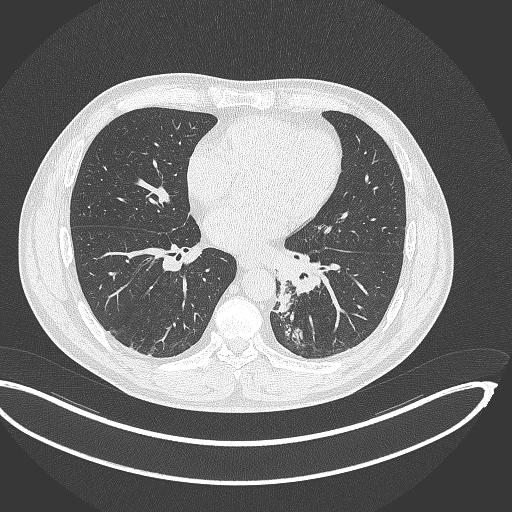
Chest CT, one axial slice; slice 154 of 362 in the series (ordered by position); reconstruction kernel B70f; lung window (W 1500 / L -600 HU); 1 mm slice thickness; 512 × 512 image matrix, field of view 442 × 442 mm. Patient: male, 50 years. From the clinical record (not read from this slice): clinical TNM (as recorded): T2a N3 M0.
Outlined on this slice (rectangle marked by the reading radiologist):
- lung tumour (recorded histology: squamous cell carcinoma): box from (x=275, y=285) to (x=295, y=319) px